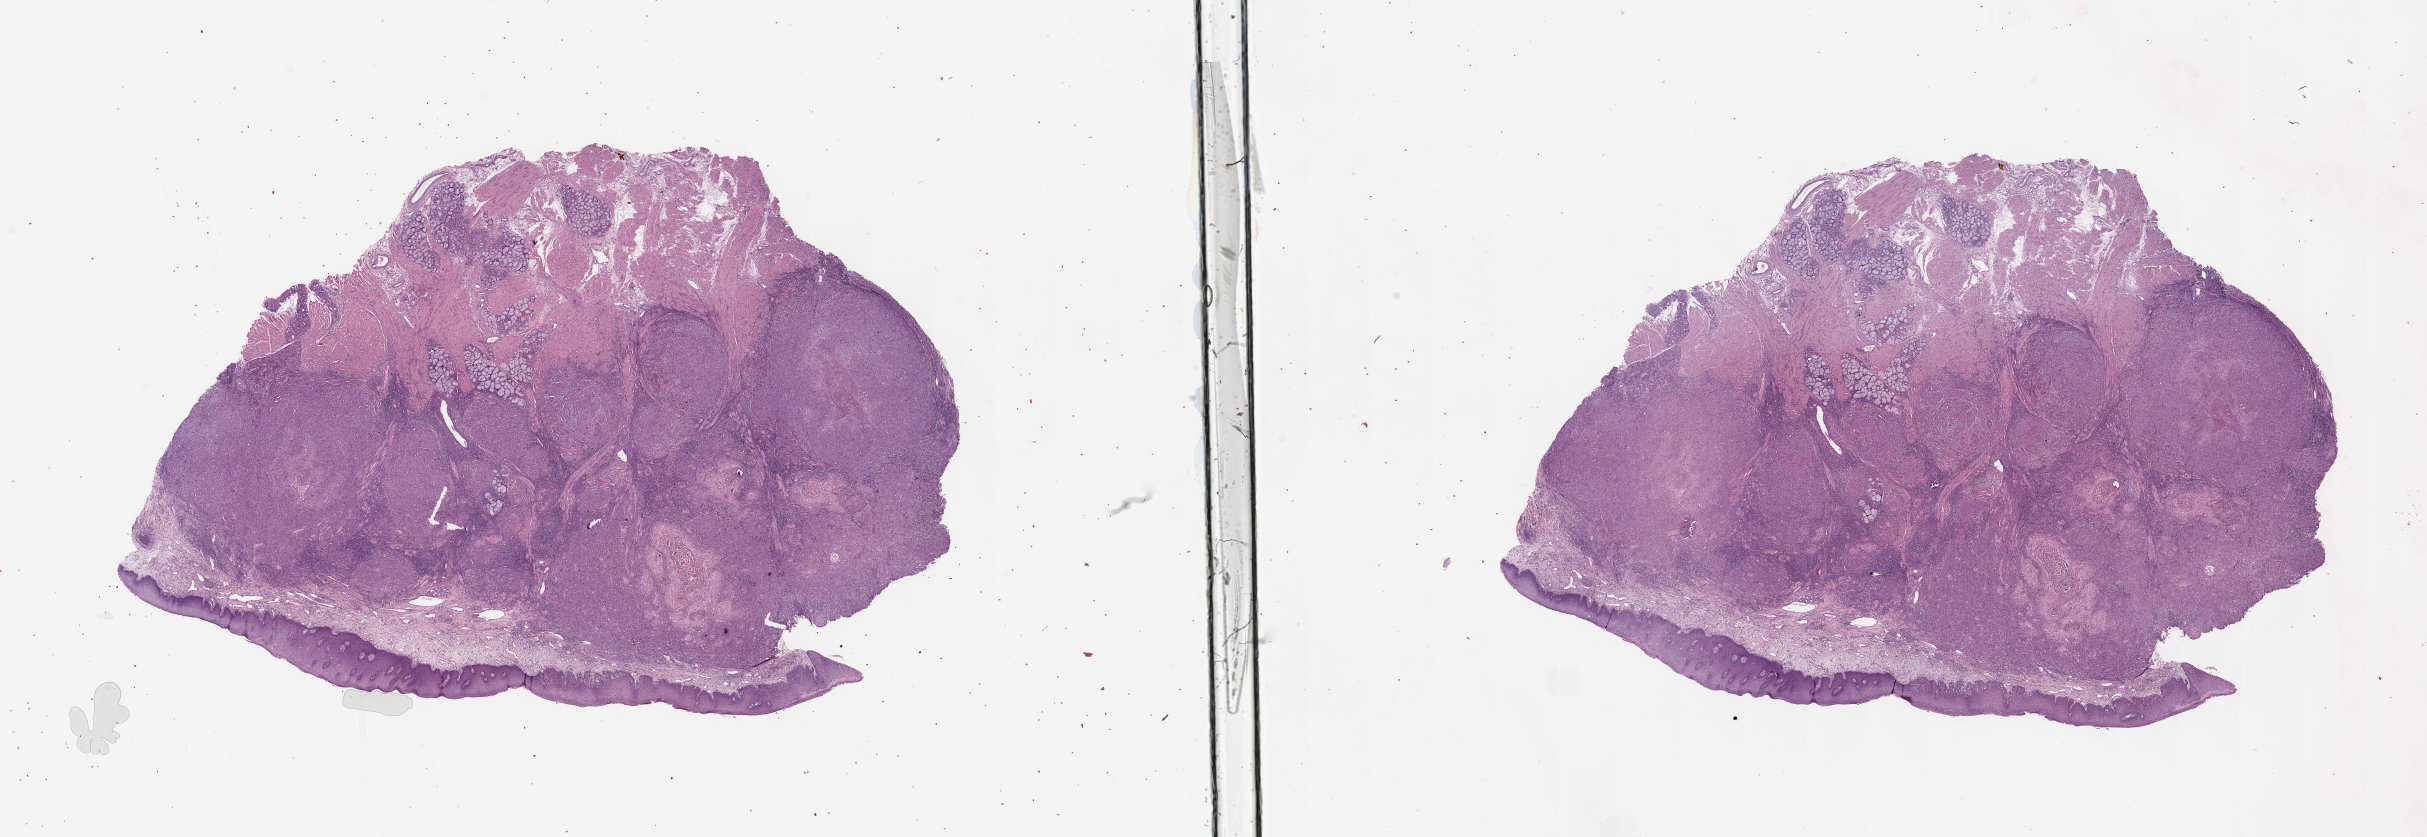
Digitized H&E tissue section (whole slide), whole scanned area (about 38.4 x 13.2 mm) shown as a low-resolution overview; head and neck, tissue type not recorded. 23-year-old male patient.
Patient diagnosis: Squamous cell carcinoma, NOS (tongue, NOS).